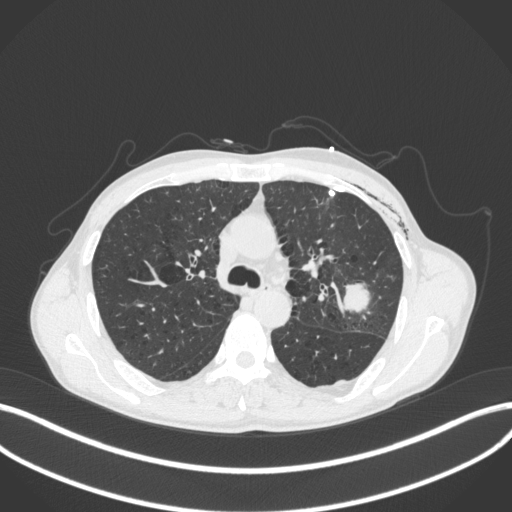
Chest CT, one axial slice; position 268 of 416 along the scan axis; reconstruction kernel B31f; 120 kVp; lung window (W 1500 / L -600 HU); 512 × 512 image matrix, field of view 400 × 400 mm. Patient: male, 58 years. From the clinical record (not read from this slice): clinical TNM (as recorded): T3 N0 M0.
Annotated regions visible in this slice (rectangle marked by the reading radiologist):
- lung tumour (recorded histology: adenocarcinoma): bounding box <342,276,374,318> (left, top, right, bottom; pixels)